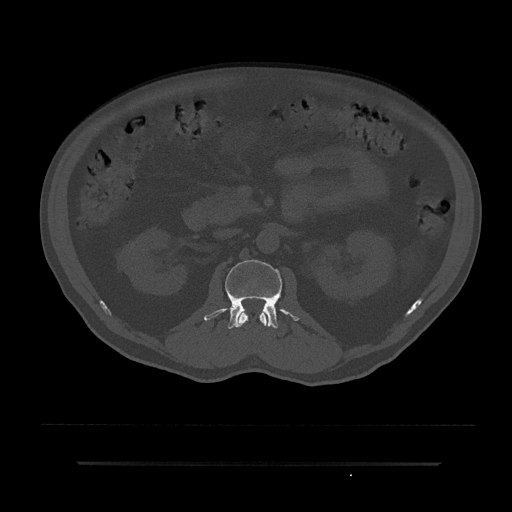
CT including the spine, one axial slice; position 96 of 797 along the scan axis; reconstruction kernel Br40s/3; 120 kVp; bone window (W 1800 / L 400 HU); 0.5 mm slice thickness; 512 × 512 image matrix, field of view 464 × 464 mm. Patient: male, 59 years. Case-level facts recorded for this patient, not image findings: primary cancer: bile ducts.
Structures marked on this image (semi-automatic segmentation, software-assisted and operator-edited):
- L1 vertebra: box from (x=238, y=311) to (x=267, y=327) px
- L2 vertebra: (x=204, y=260)–(x=299, y=329)